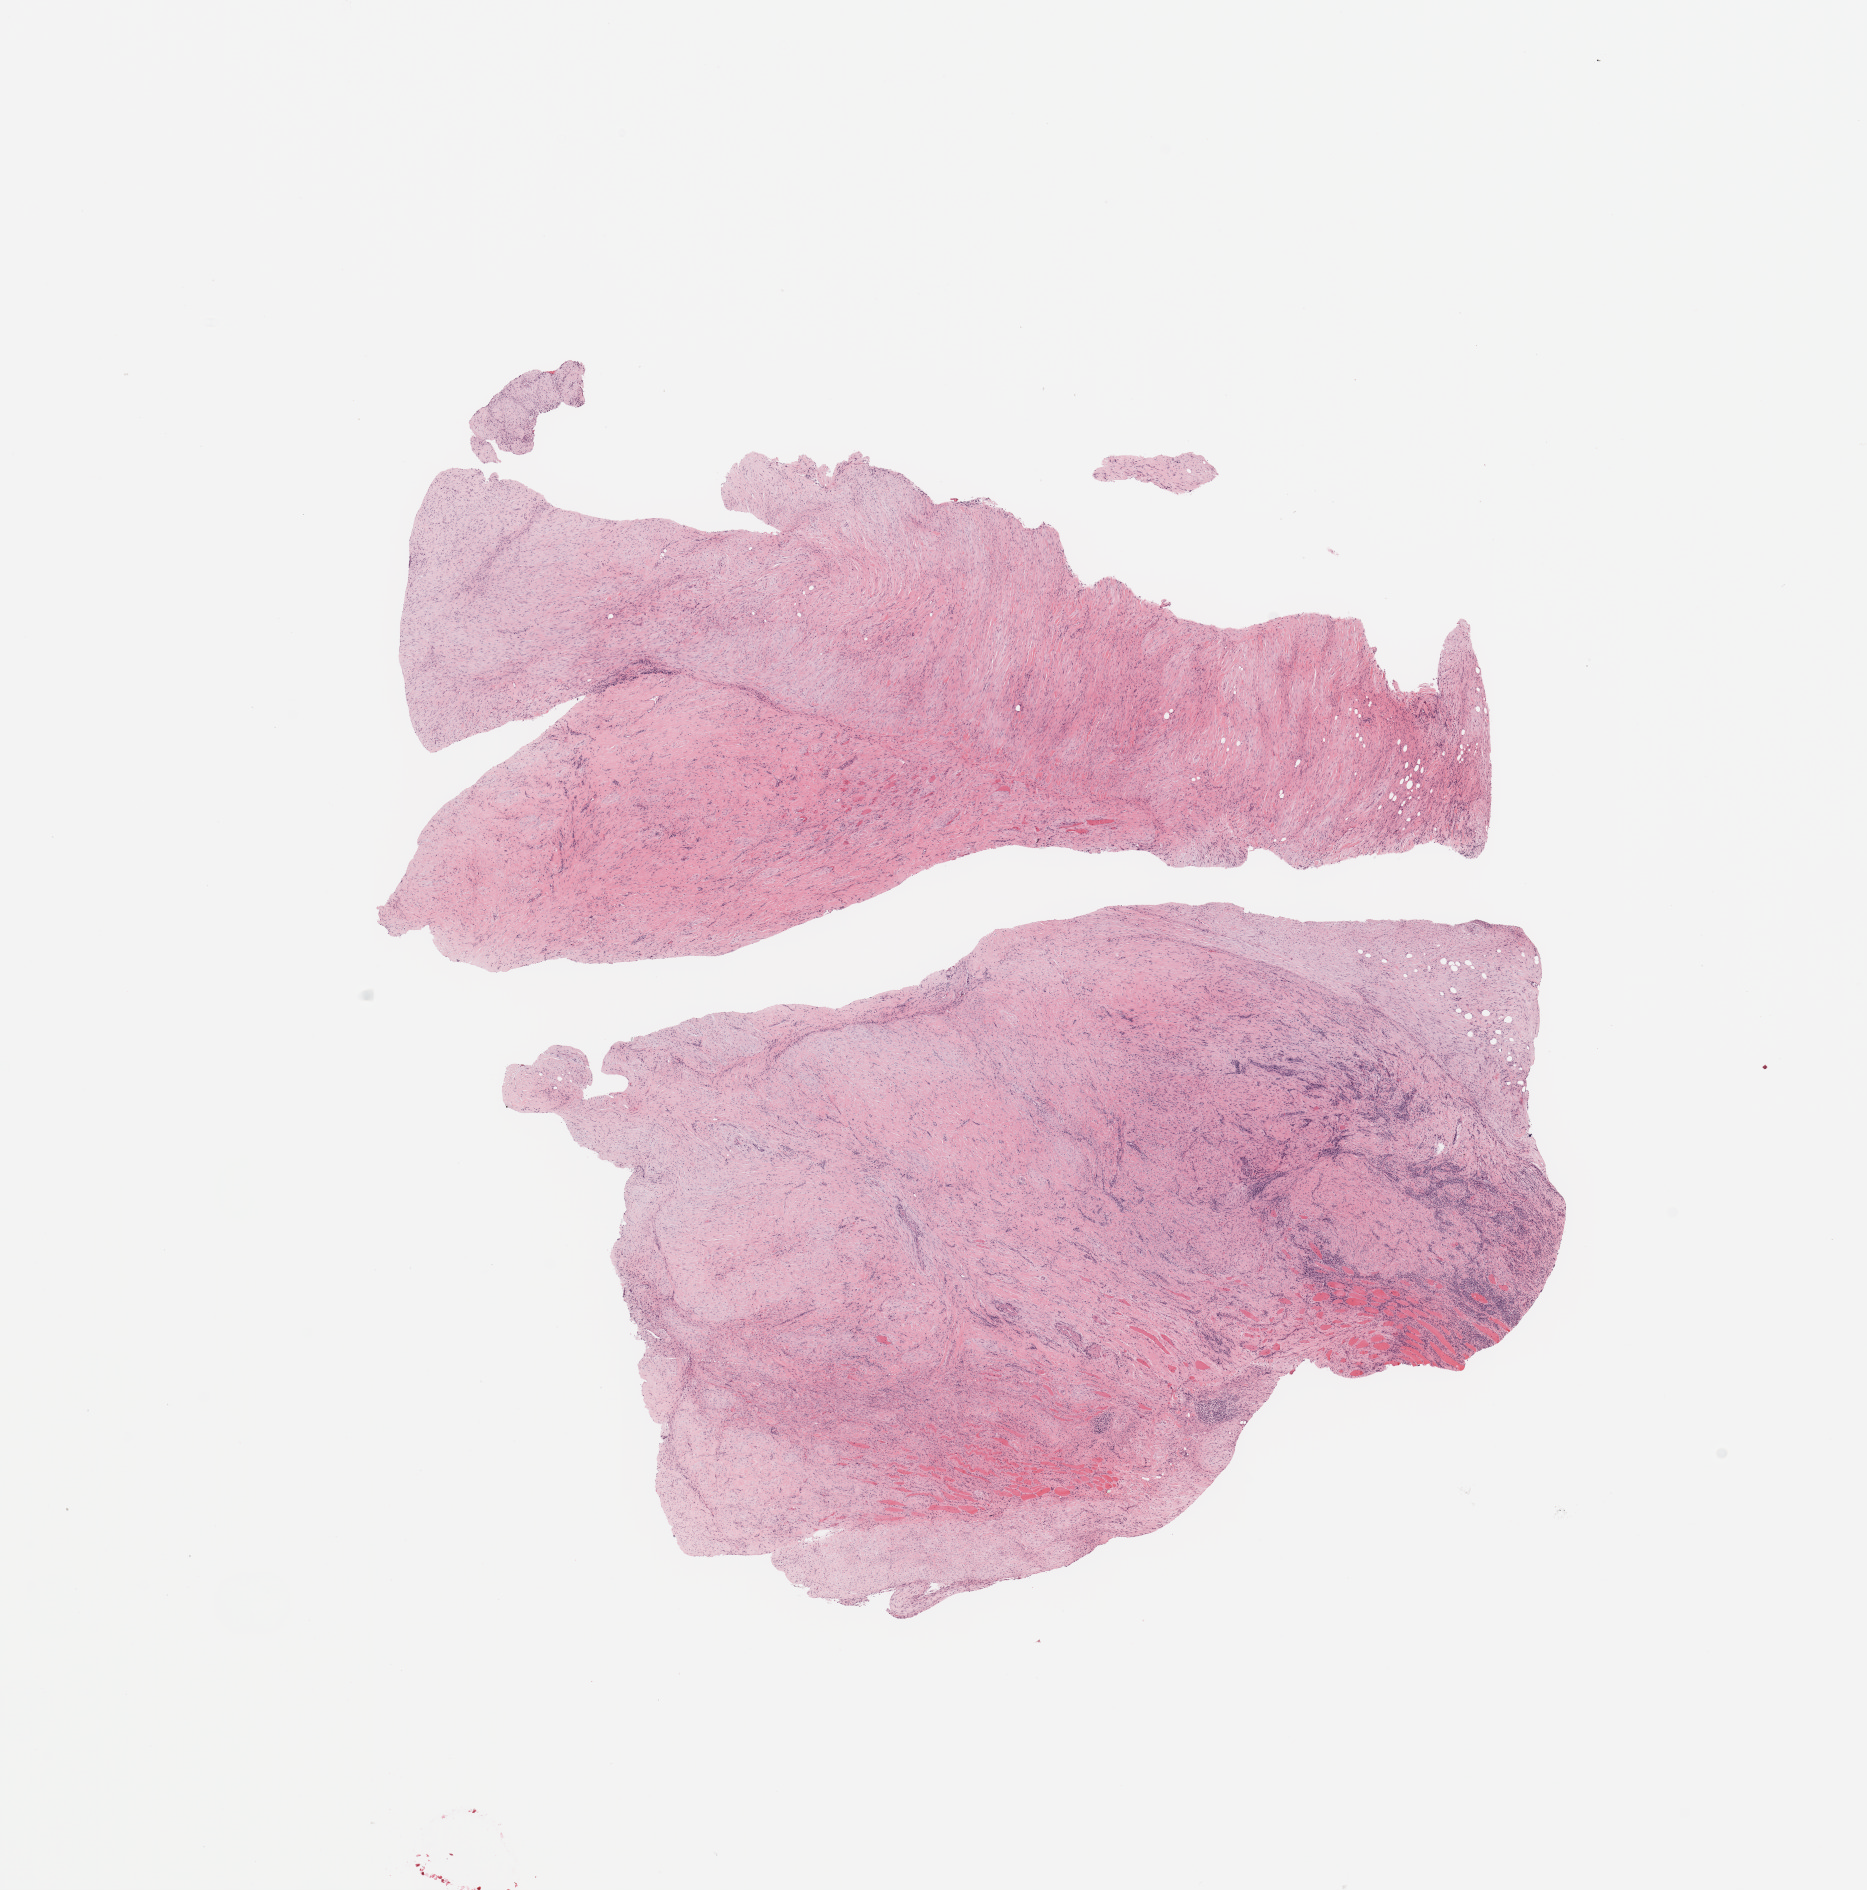
Hematoxylin and eosin (H&E) stained whole-slide image, a low-resolution overview of the entire scanned area, about 14.8 x 14.9 mm (slide scanned at 20x), tumour tissue sample. Patient: female, age 80 years.
Patient diagnosis (cohort enrolment): sarcoma (site not recorded at cohort level). Primary tumour site (as recorded): lower extremity.